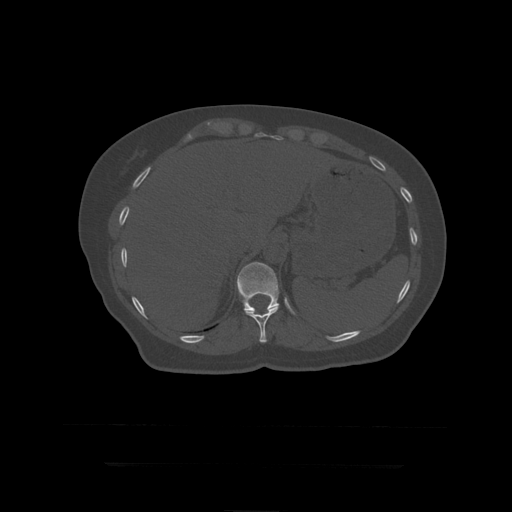
CT including the spine, one axial slice; slice 210 of 399 in the series (ordered by position); reconstruction kernel STANDARD; bone window (W 1800 / L 400 HU); 1.25 mm slice thickness; 512 × 512 image matrix, field of view 450 × 450 mm. Patient age 41 years. Case-level facts recorded for this patient, not image findings: primary cancer: breast.
Annotated regions visible in this slice (semi-automatically segmented with operator editing):
- T11 vertebra: bounding box (x1, y1, x2, y2) in pixels: (245, 305, 280, 343)
- T12 vertebra: (237, 262, 280, 312)